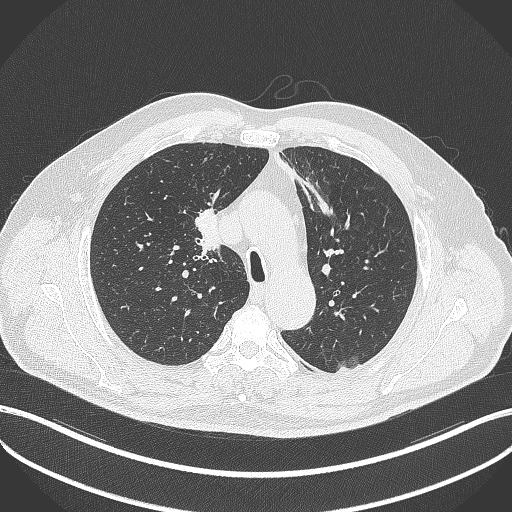
Chest CT, one axial slice. Reconstruction kernel B70f. Lung window (W 1500 / L -600 HU). 512 × 512 image matrix, field of view 400 × 400 mm. Patient: male, 60 years. Case-level facts recorded for this patient, not image findings: clinical TNM (as recorded): T1b N1 M0.
Annotated regions visible in this slice (bounding box drawn by a radiologist):
- lung tumour (recorded histology: squamous cell carcinoma): bounding box [x1, y1, x2, y2] px = [195, 209, 221, 252]